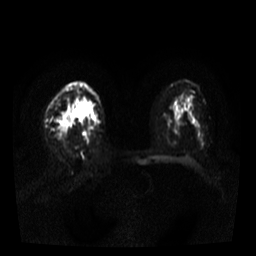
Breast MRI, one axial slice; slice 21 of 37 in the series (ordered by position); diffusion-weighted series; image 2 of 4 stored at this slice position (different b-values; order by instance number); 3 T; 5 mm slice thickness; 256 × 256 image matrix, field of view 320 × 320 mm. Female patient.
Structures marked on this image (outlined manually by an expert reader):
- tumour on diffusion-weighted imaging: bounding box (x1, y1, x2, y2) in pixels: (56, 111, 71, 136)